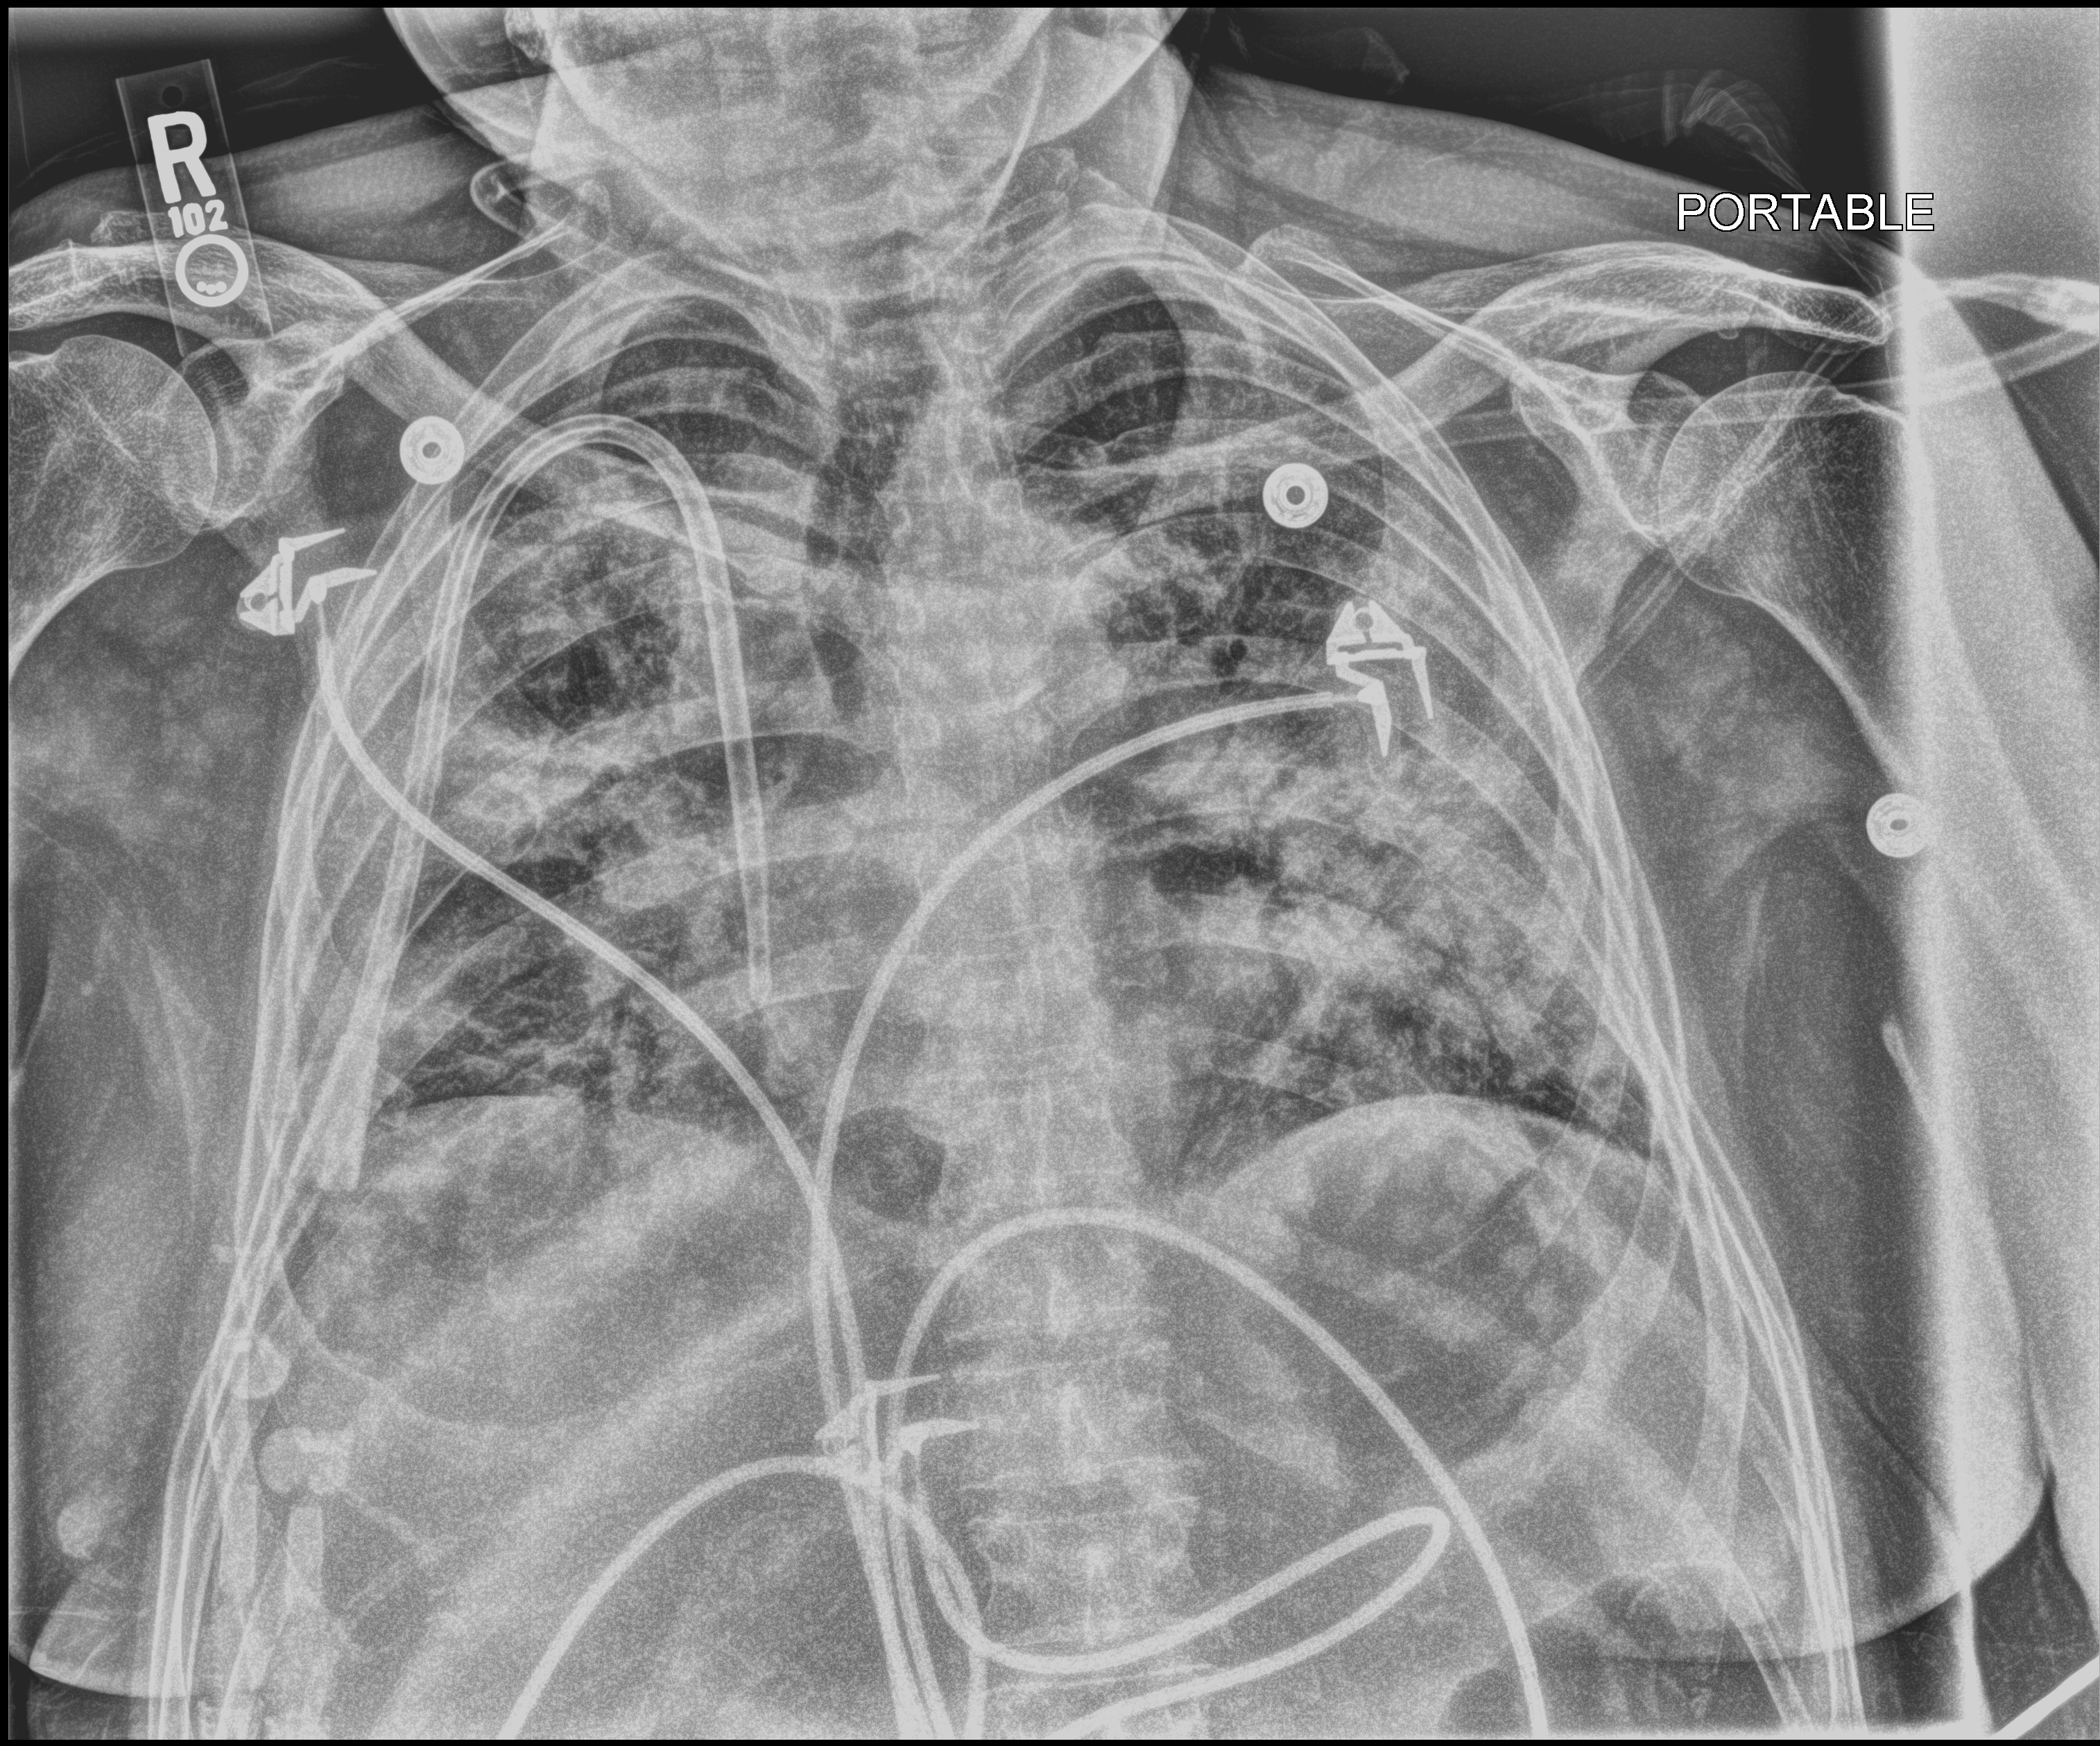
Bedside chest radiograph (computed radiography); anteroposterior (AP) projection. Male patient hospitalised with COVID-19, age 60–74 years.
From the hospital-stay record, not from the radiograph (when in the stay this image was taken is not recorded): admitted to intensive care during this hospital stay: no.